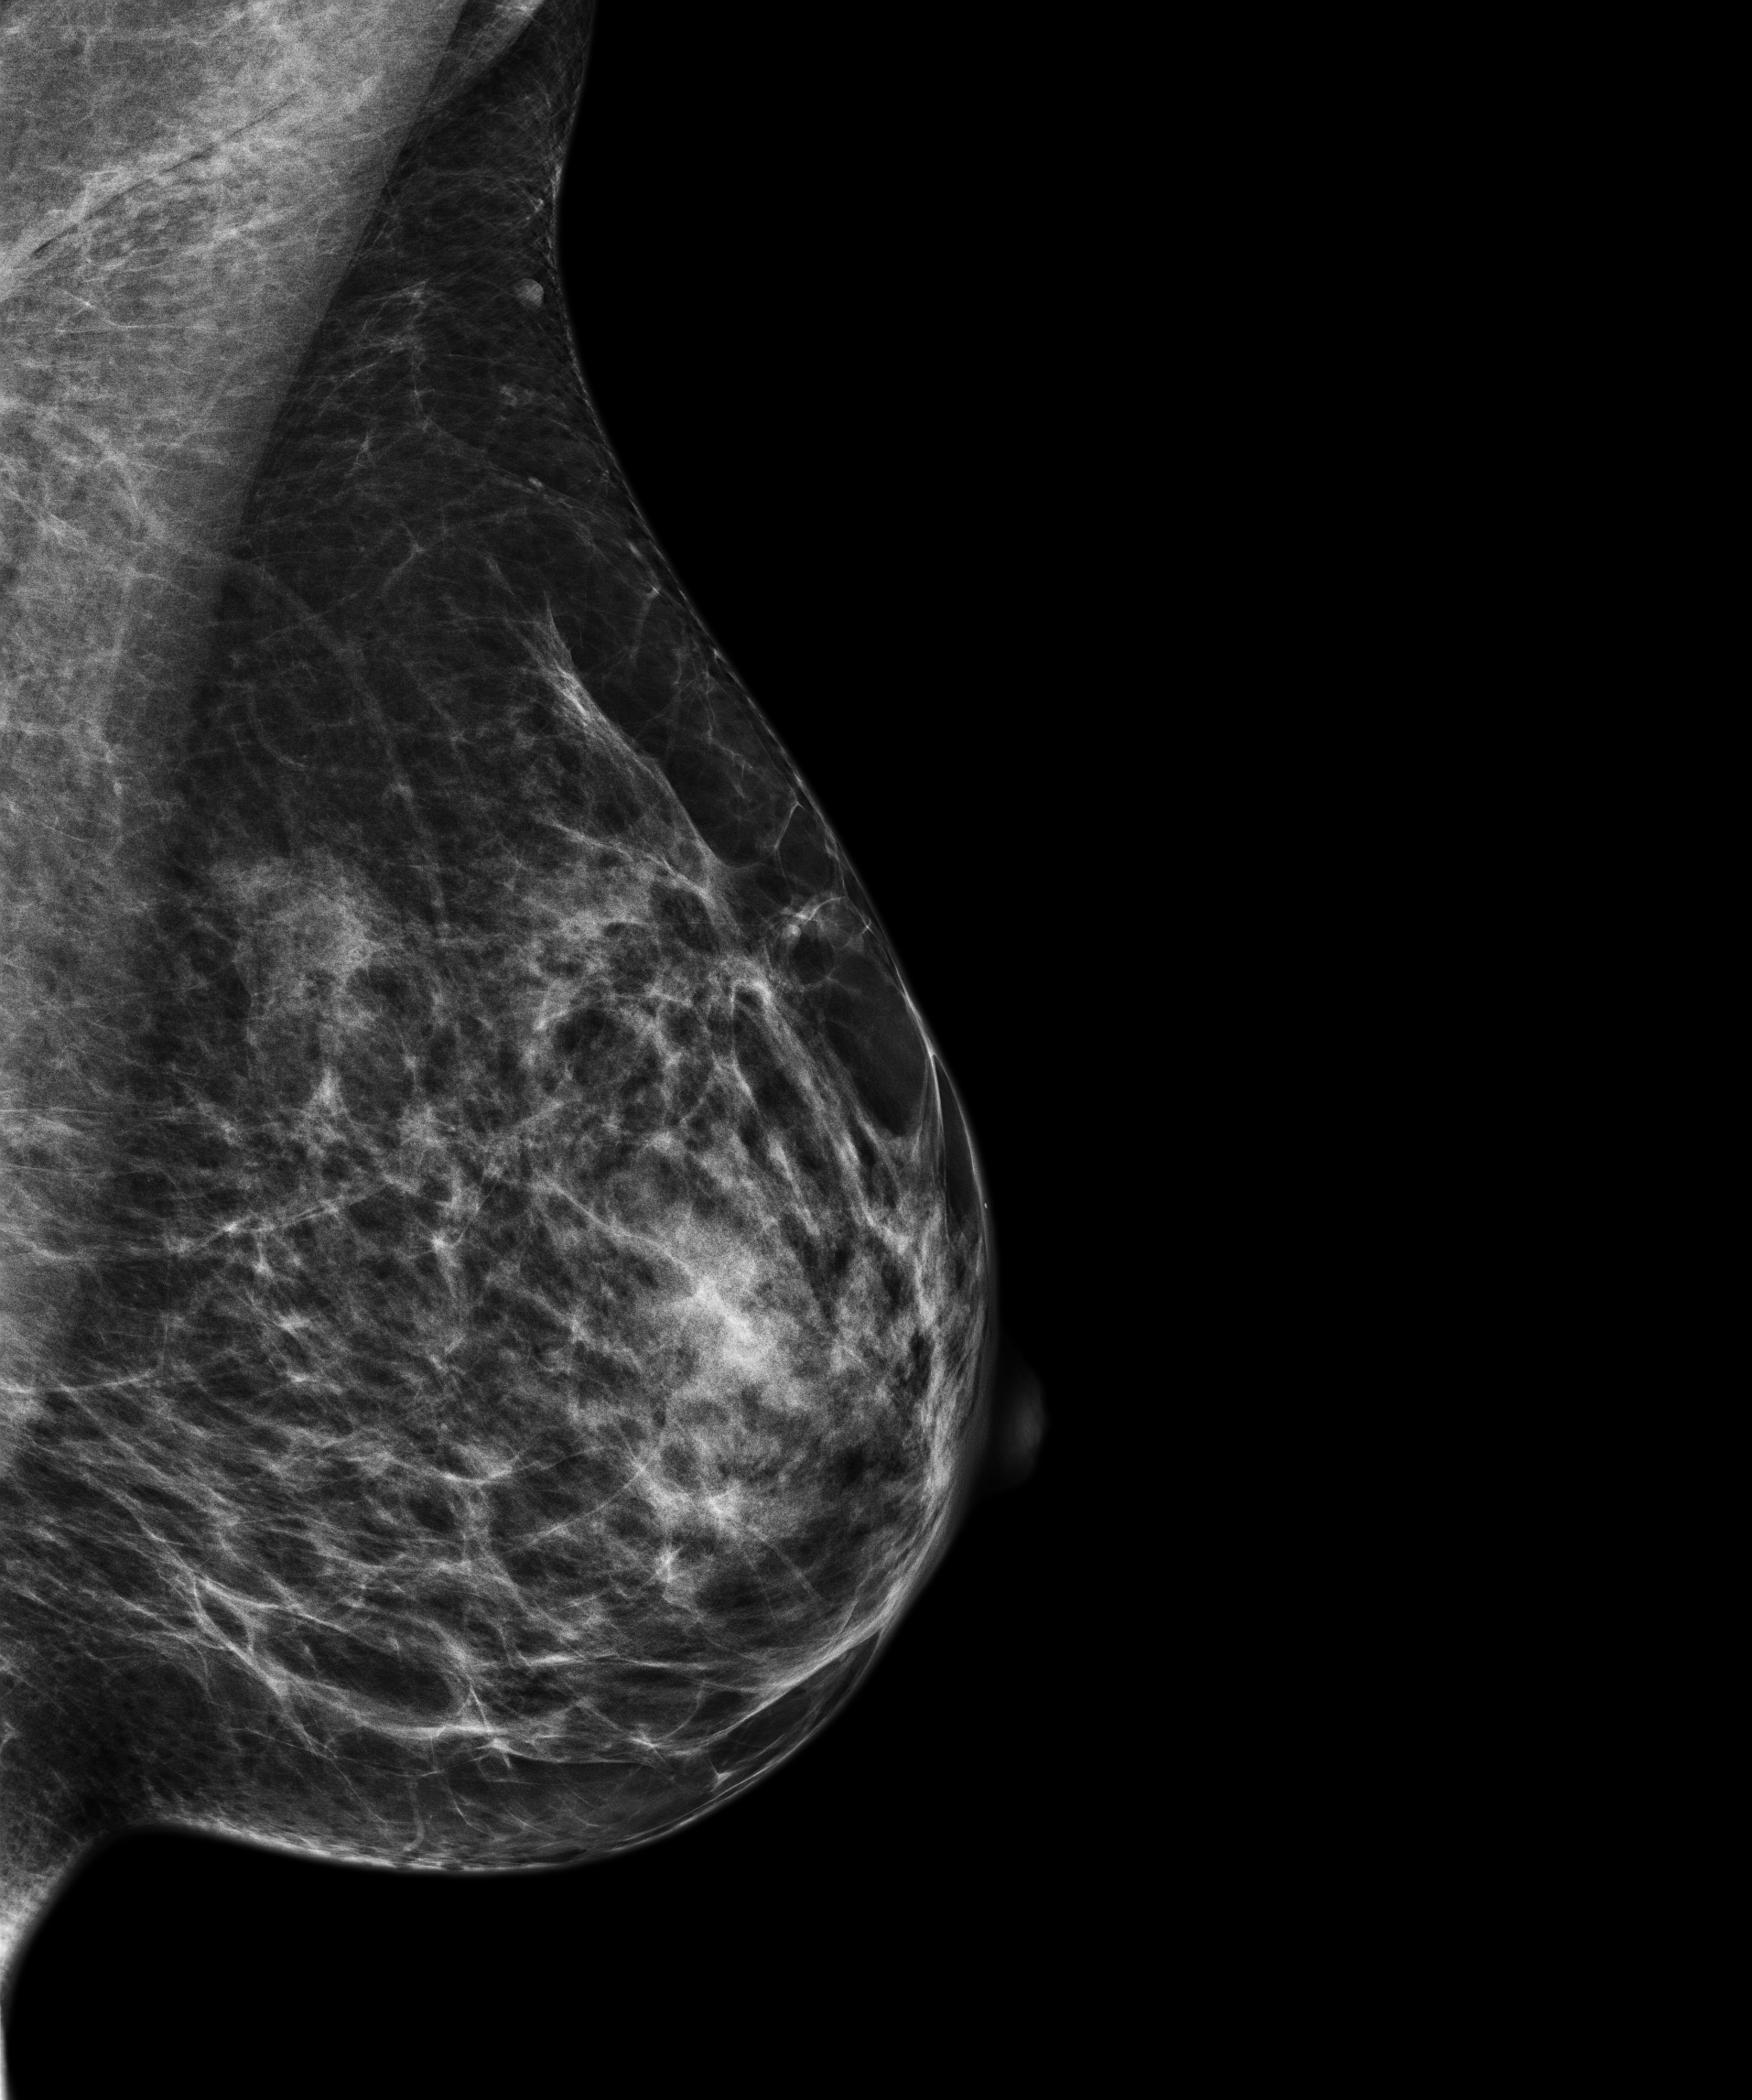
Screening examination; compressed breast thickness 56.5 mm; system: Senographe Pristina. Patient: female, 57 years.
Image type: full-field digital mammogram. Breast: left. Projection: medio-lateral oblique projection.